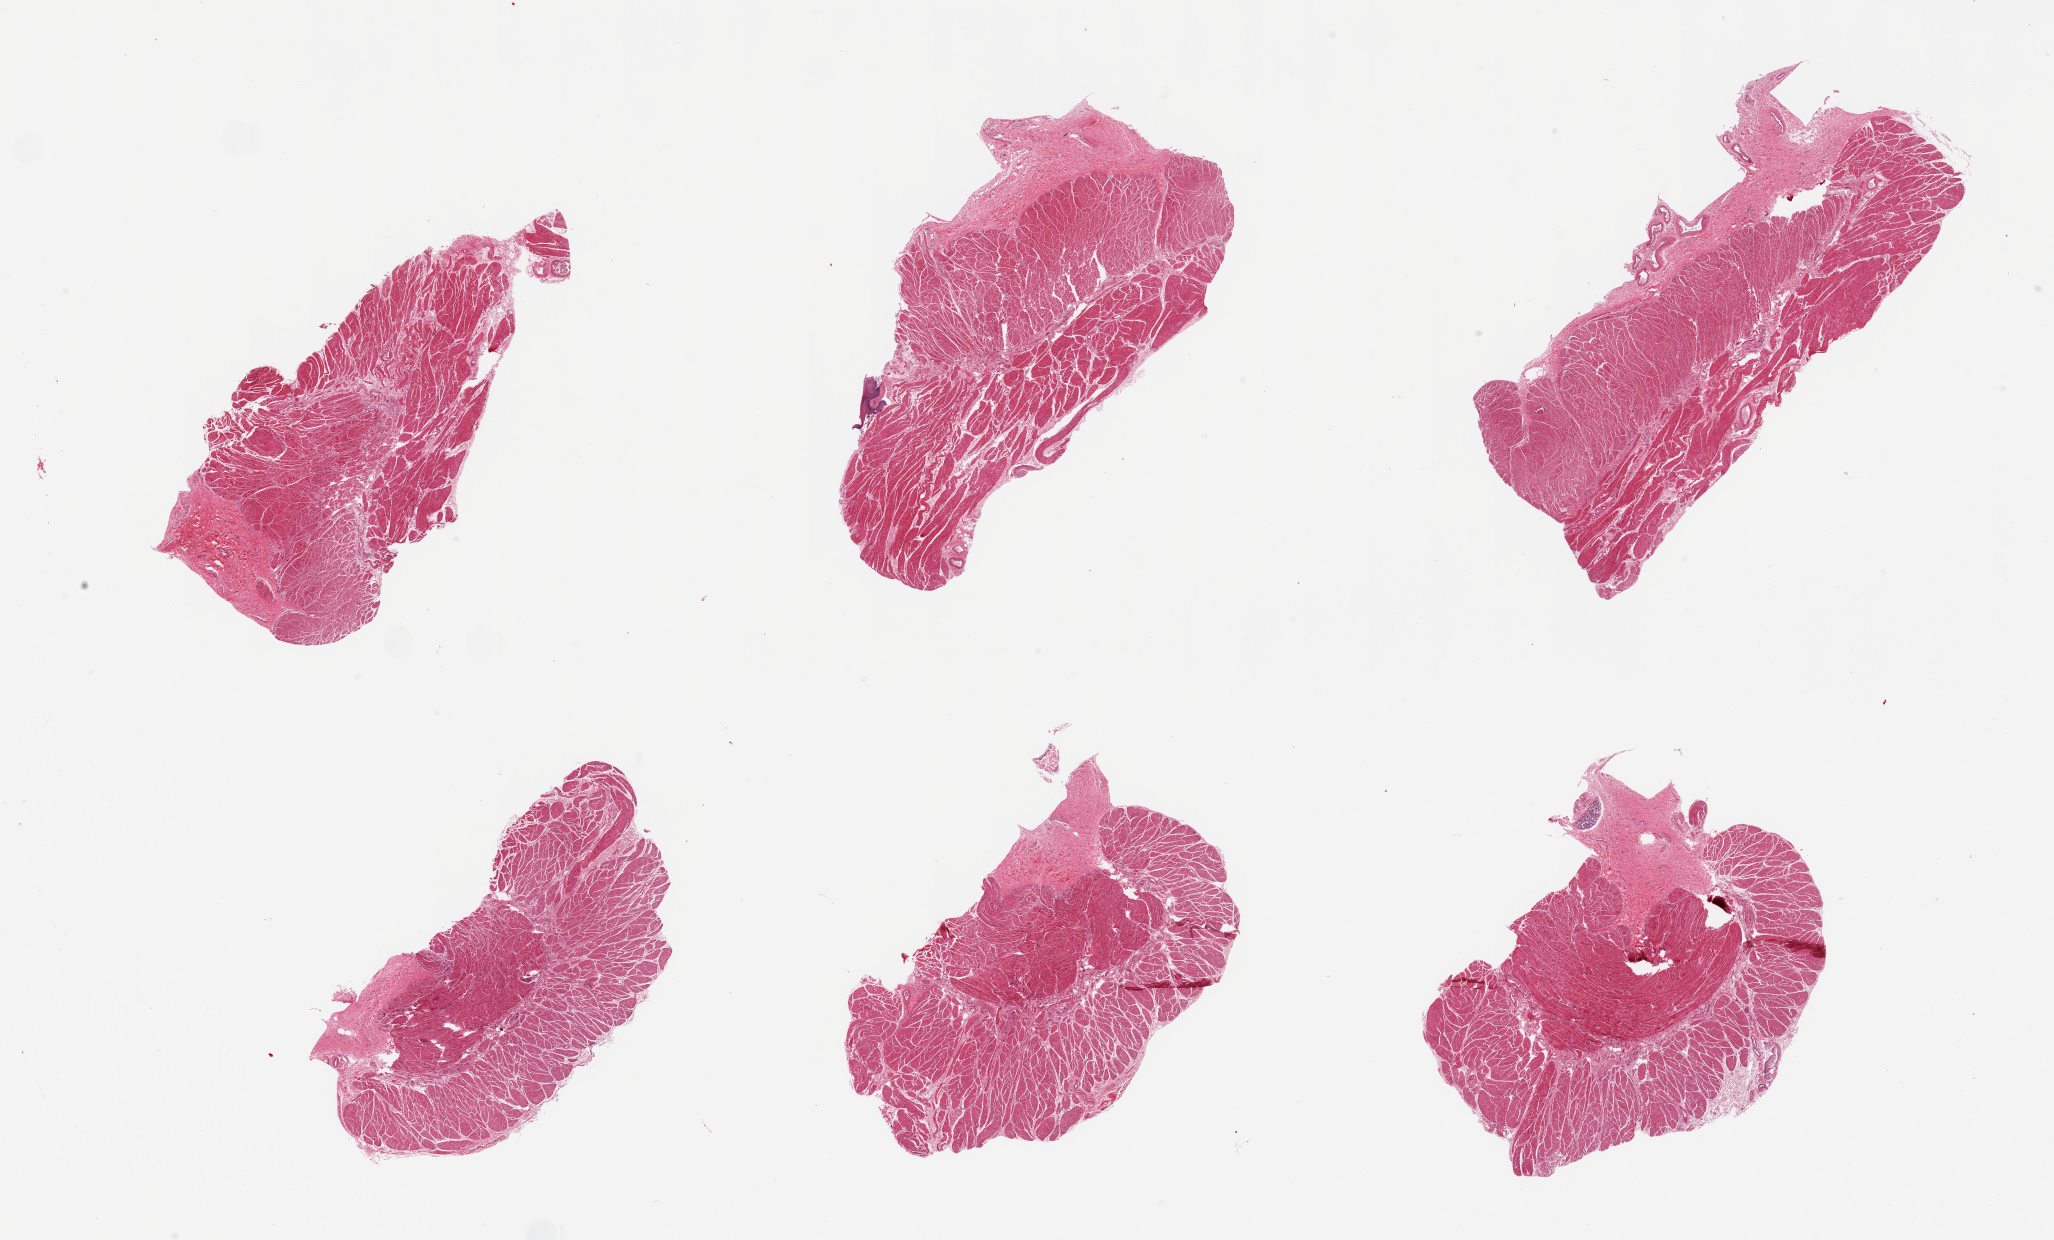
Whole-slide image, hematoxylin and eosin (H&E) stain — low-resolution overview of the scanned area, about 32.5 x 19.6 mm; PAXgene-fixed, paraffin-embedded tissue; sampled site (target tissue): esophageal muscle; donor tissue sample. Female donor.
* reviewer comment on this tissue sample: 6 pieces, well dissected